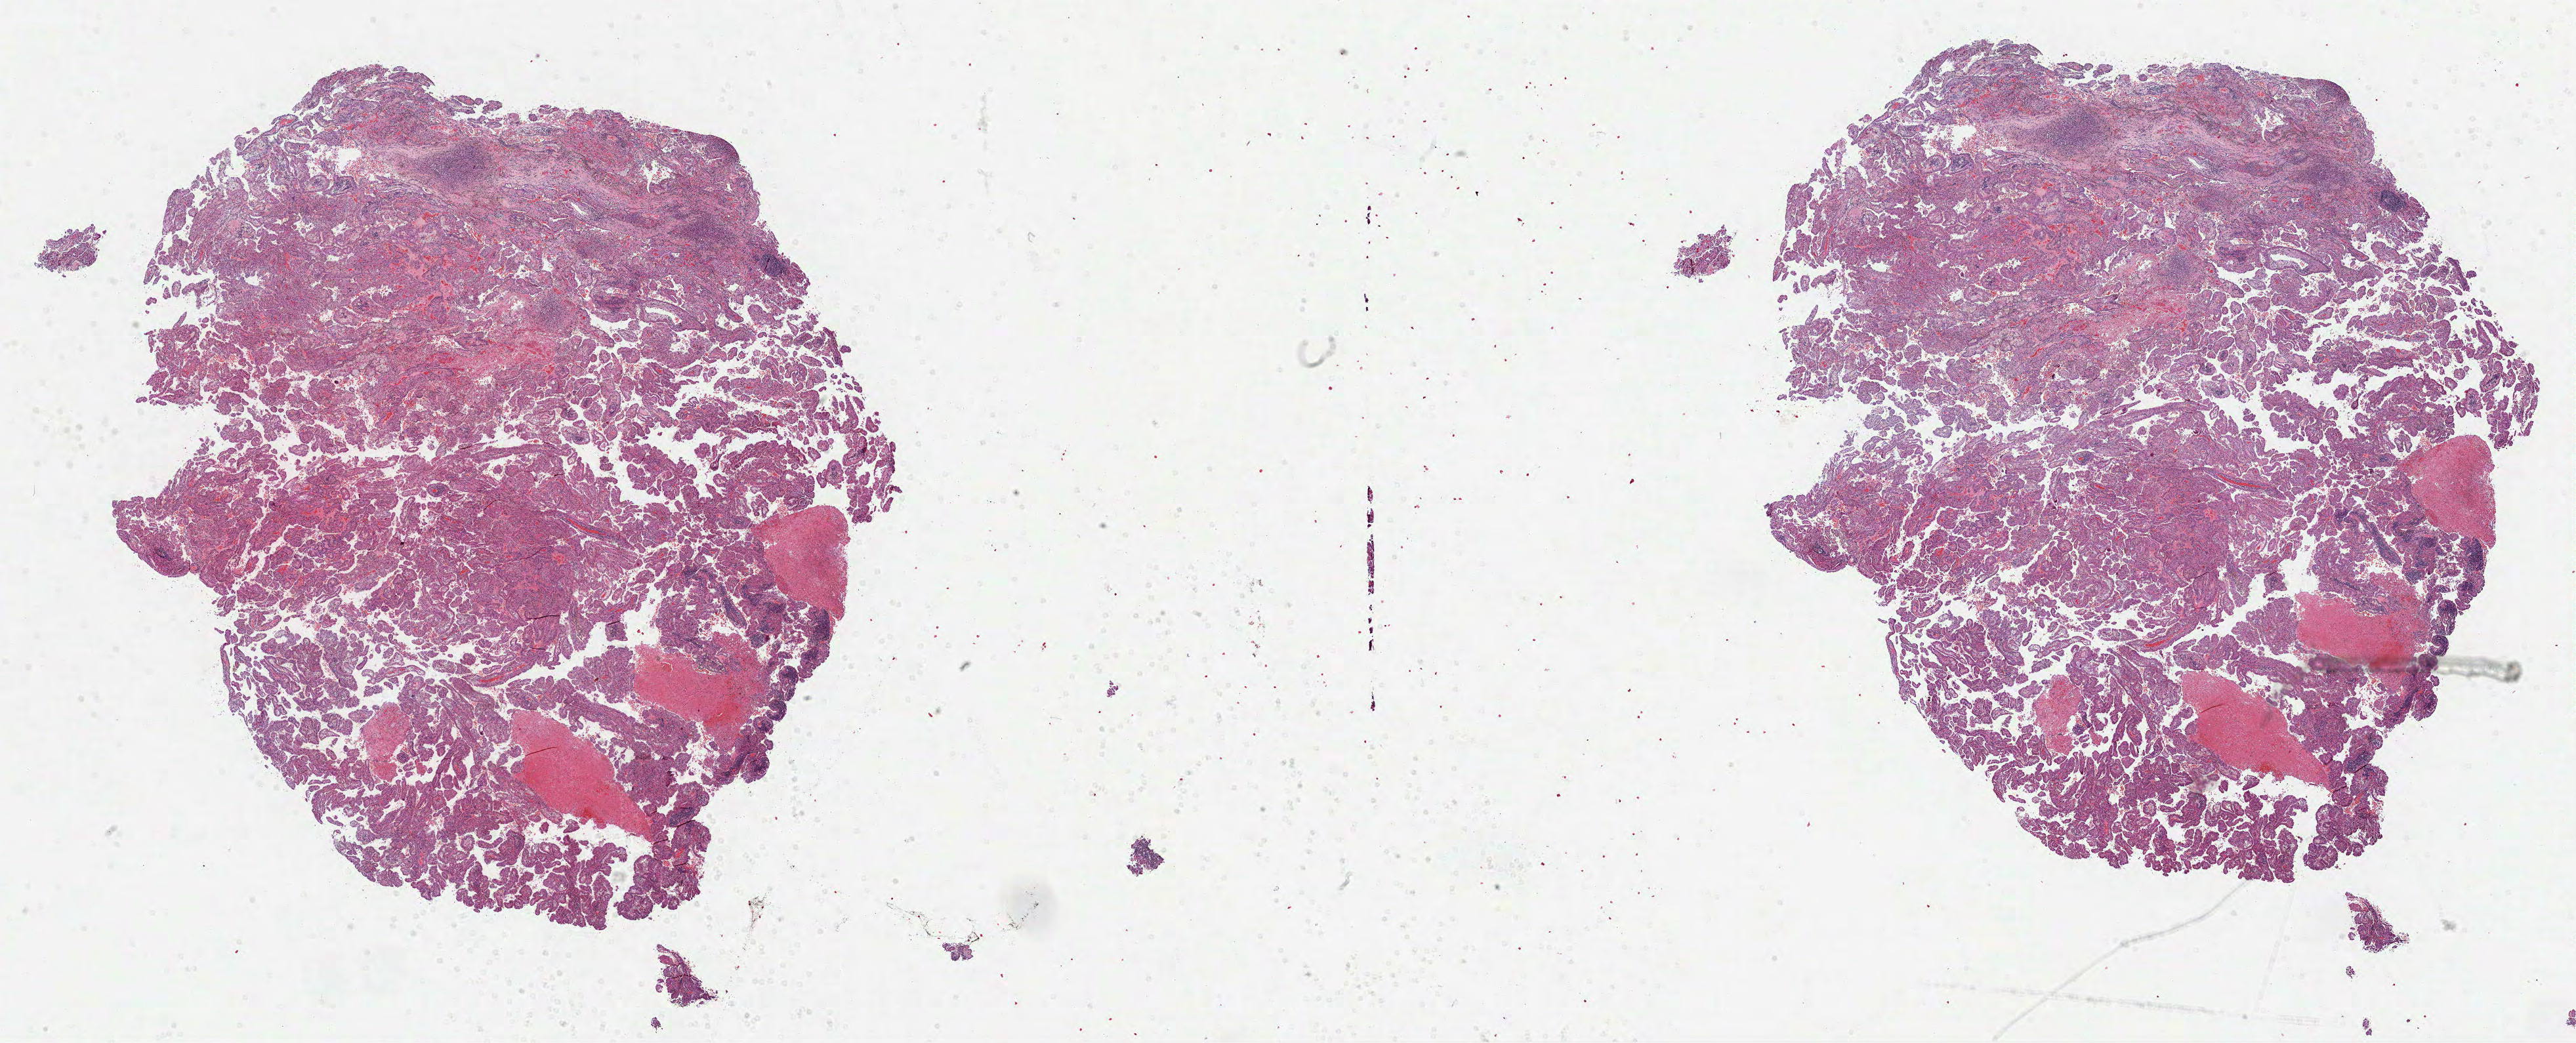
Whole-slide histology image, Hematoxylin and eosin (H&E) stained — a low-resolution overview of the entire scanned area, about 31.7 x 12.8 mm (from a 40x scan). Formalin-fixed paraffin-embedded (FFPE) diagnostic section. Primary tumour sample from the kidney. Female, age 72 years at initial diagnosis. Histologic grade: G2 (moderately differentiated).
- laterality: left
- pathologic diagnosis: Clear cell adenocarcinoma, NOS
- AJCC pathologic stage: I